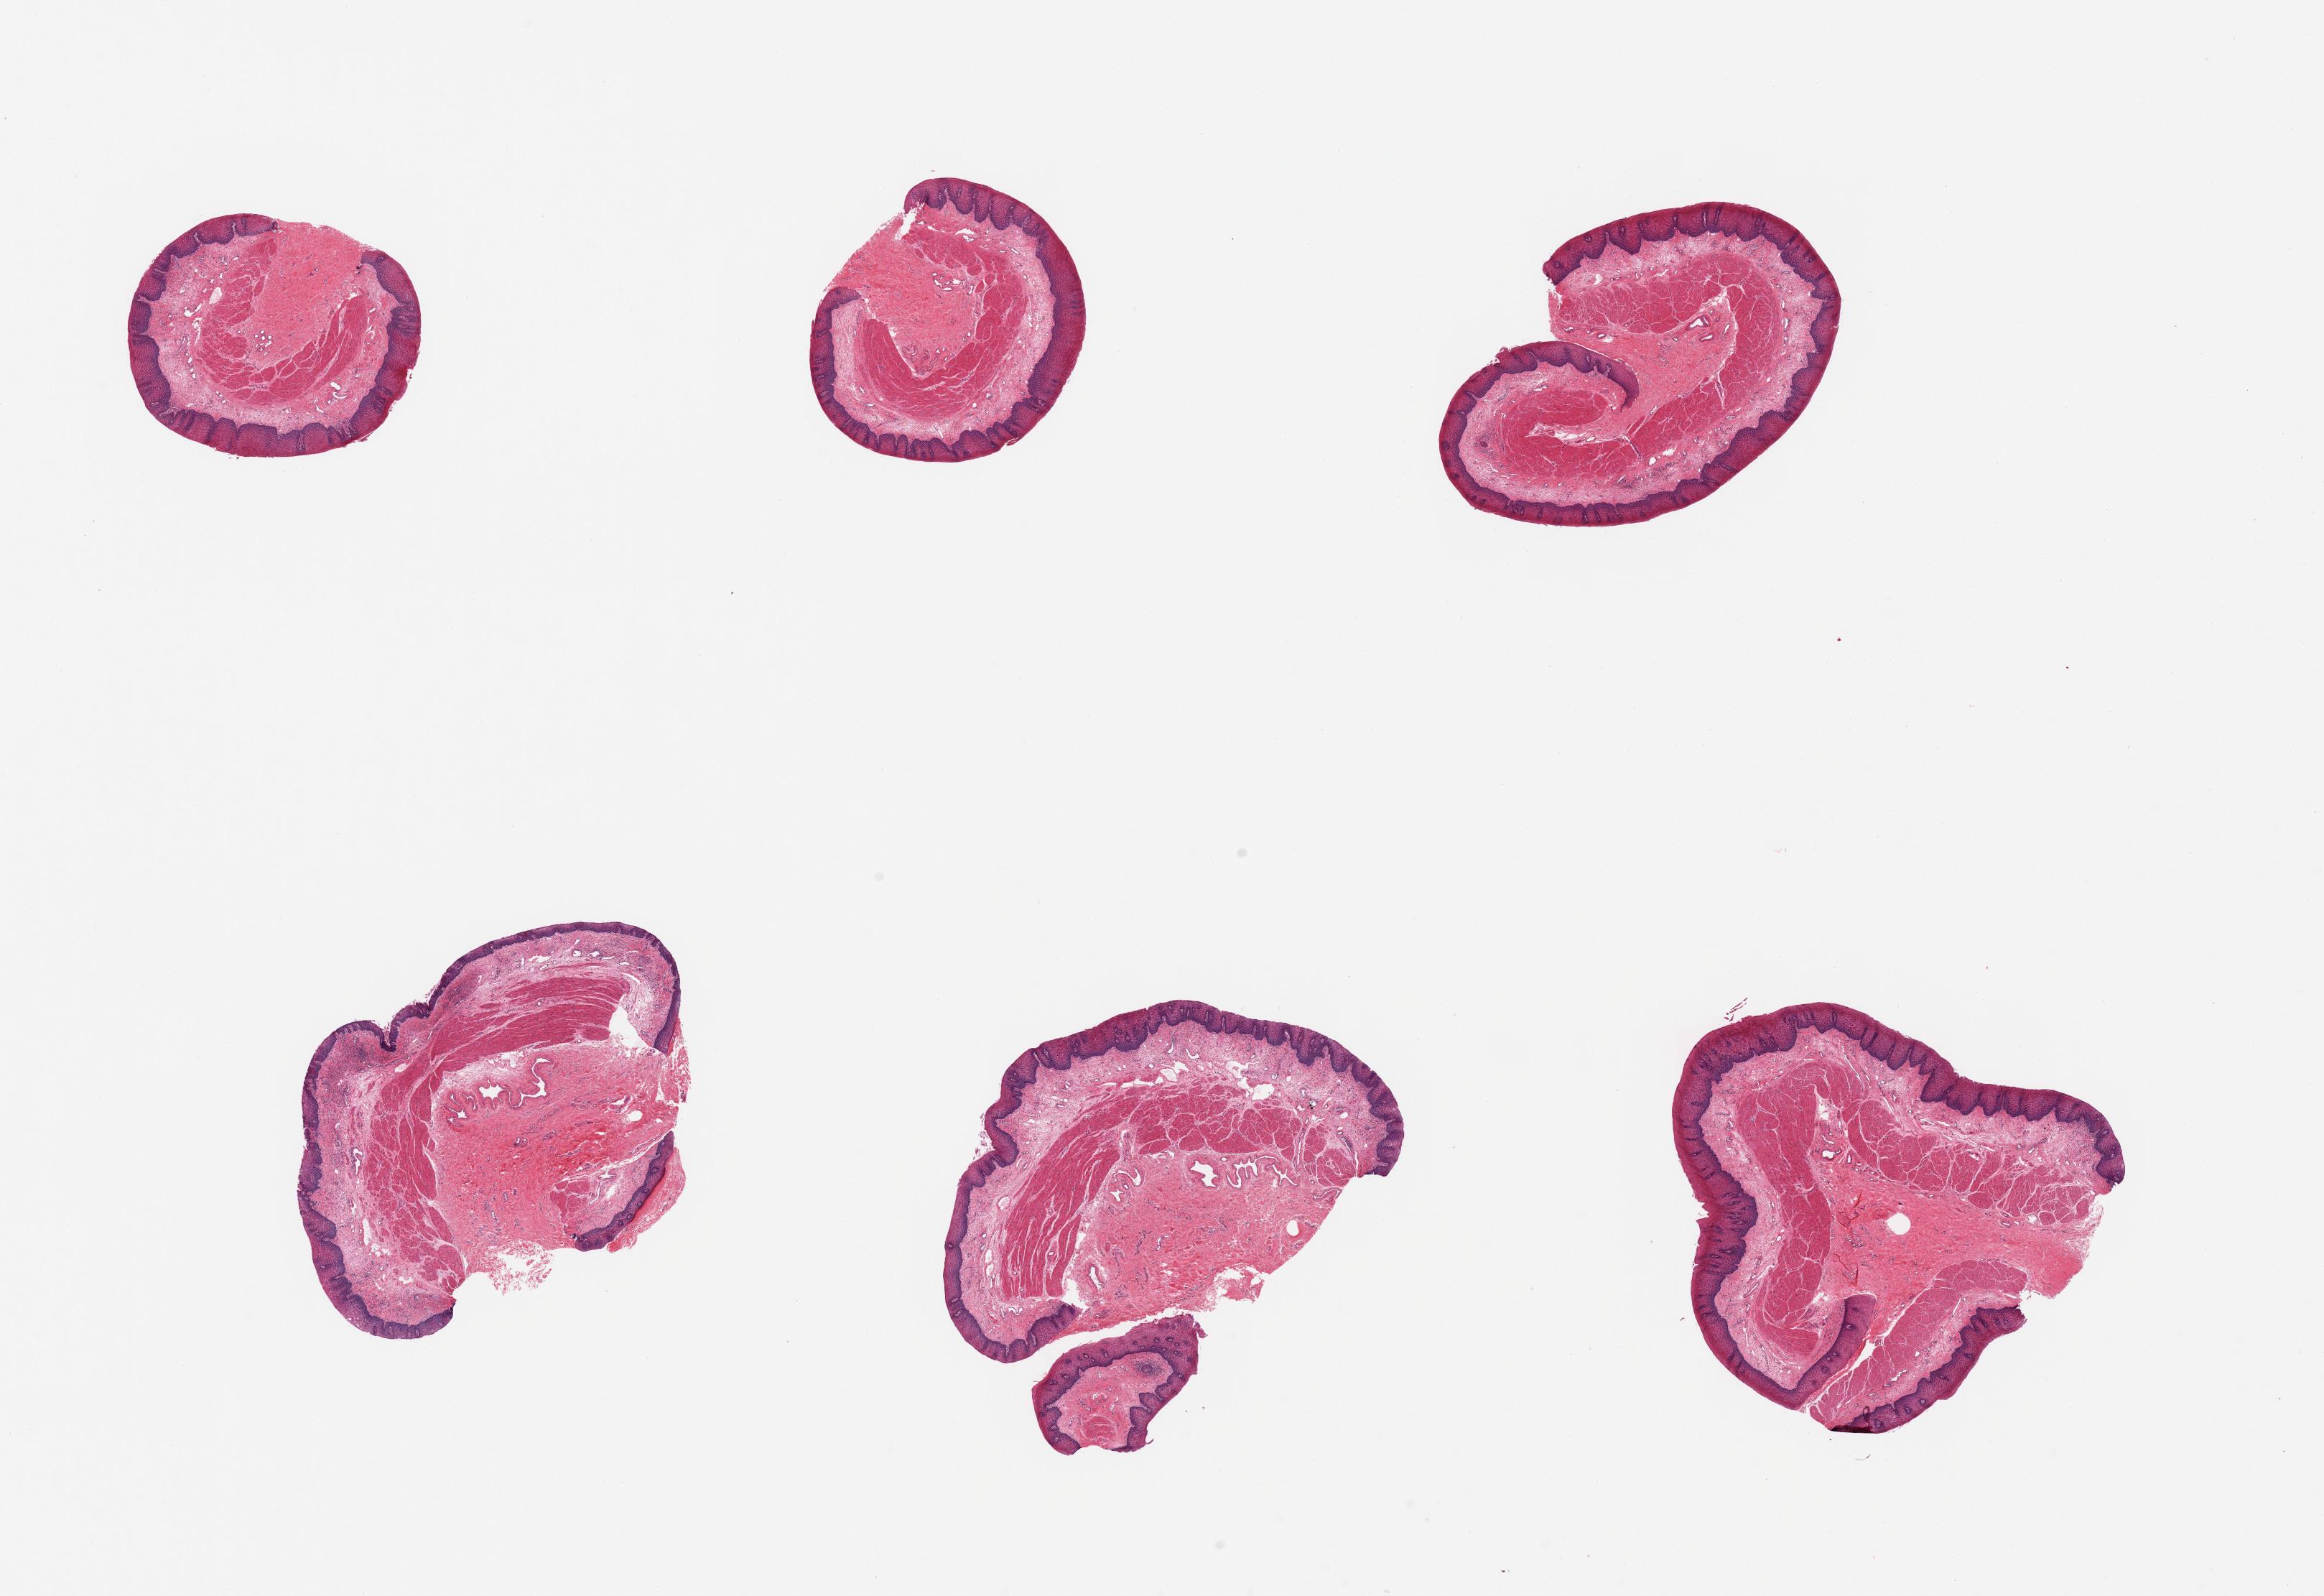
Whole-slide image, H&E stain — whole scanned area (about 25.6 x 17.6 mm) shown as a low-resolution overview, PAXgene-fixed, paraffin-embedded tissue, target tissue: esophageal mucous membrane, tissue donor sample.
* reviewer comment on this tissue sample: 6 pieces; squamous mucosa is ~10% thickness